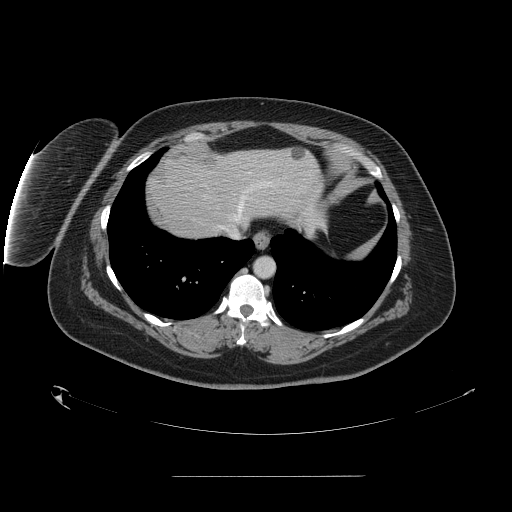
Contrast-enhanced abdominal CT, one axial slice. Slice 136 of 164 in the series (ordered by position). Intravenous contrast given. Soft-tissue window (W 400 / L 40 HU). 2.5 mm slice thickness. 512 × 512 image matrix, field of view 495 × 495 mm. Female patient, age 52 years. From the clinical record (not read from this slice): diagnosis: colorectal cancer liver metastases, imaged before liver resection; multiple liver metastases: yes; largest metastasis: 3.5 cm; chemotherapy before resection: no.
Structures marked on this image (manually delineated by an expert):
- hepatic veins: bounding box <219,183,272,239> (left, top, right, bottom; pixels)
- liver: <148,147,321,239>
- planned liver remnant (the part of the liver to remain after resection): <175,148,322,225>
- liver metastasis: <290,149,305,160>